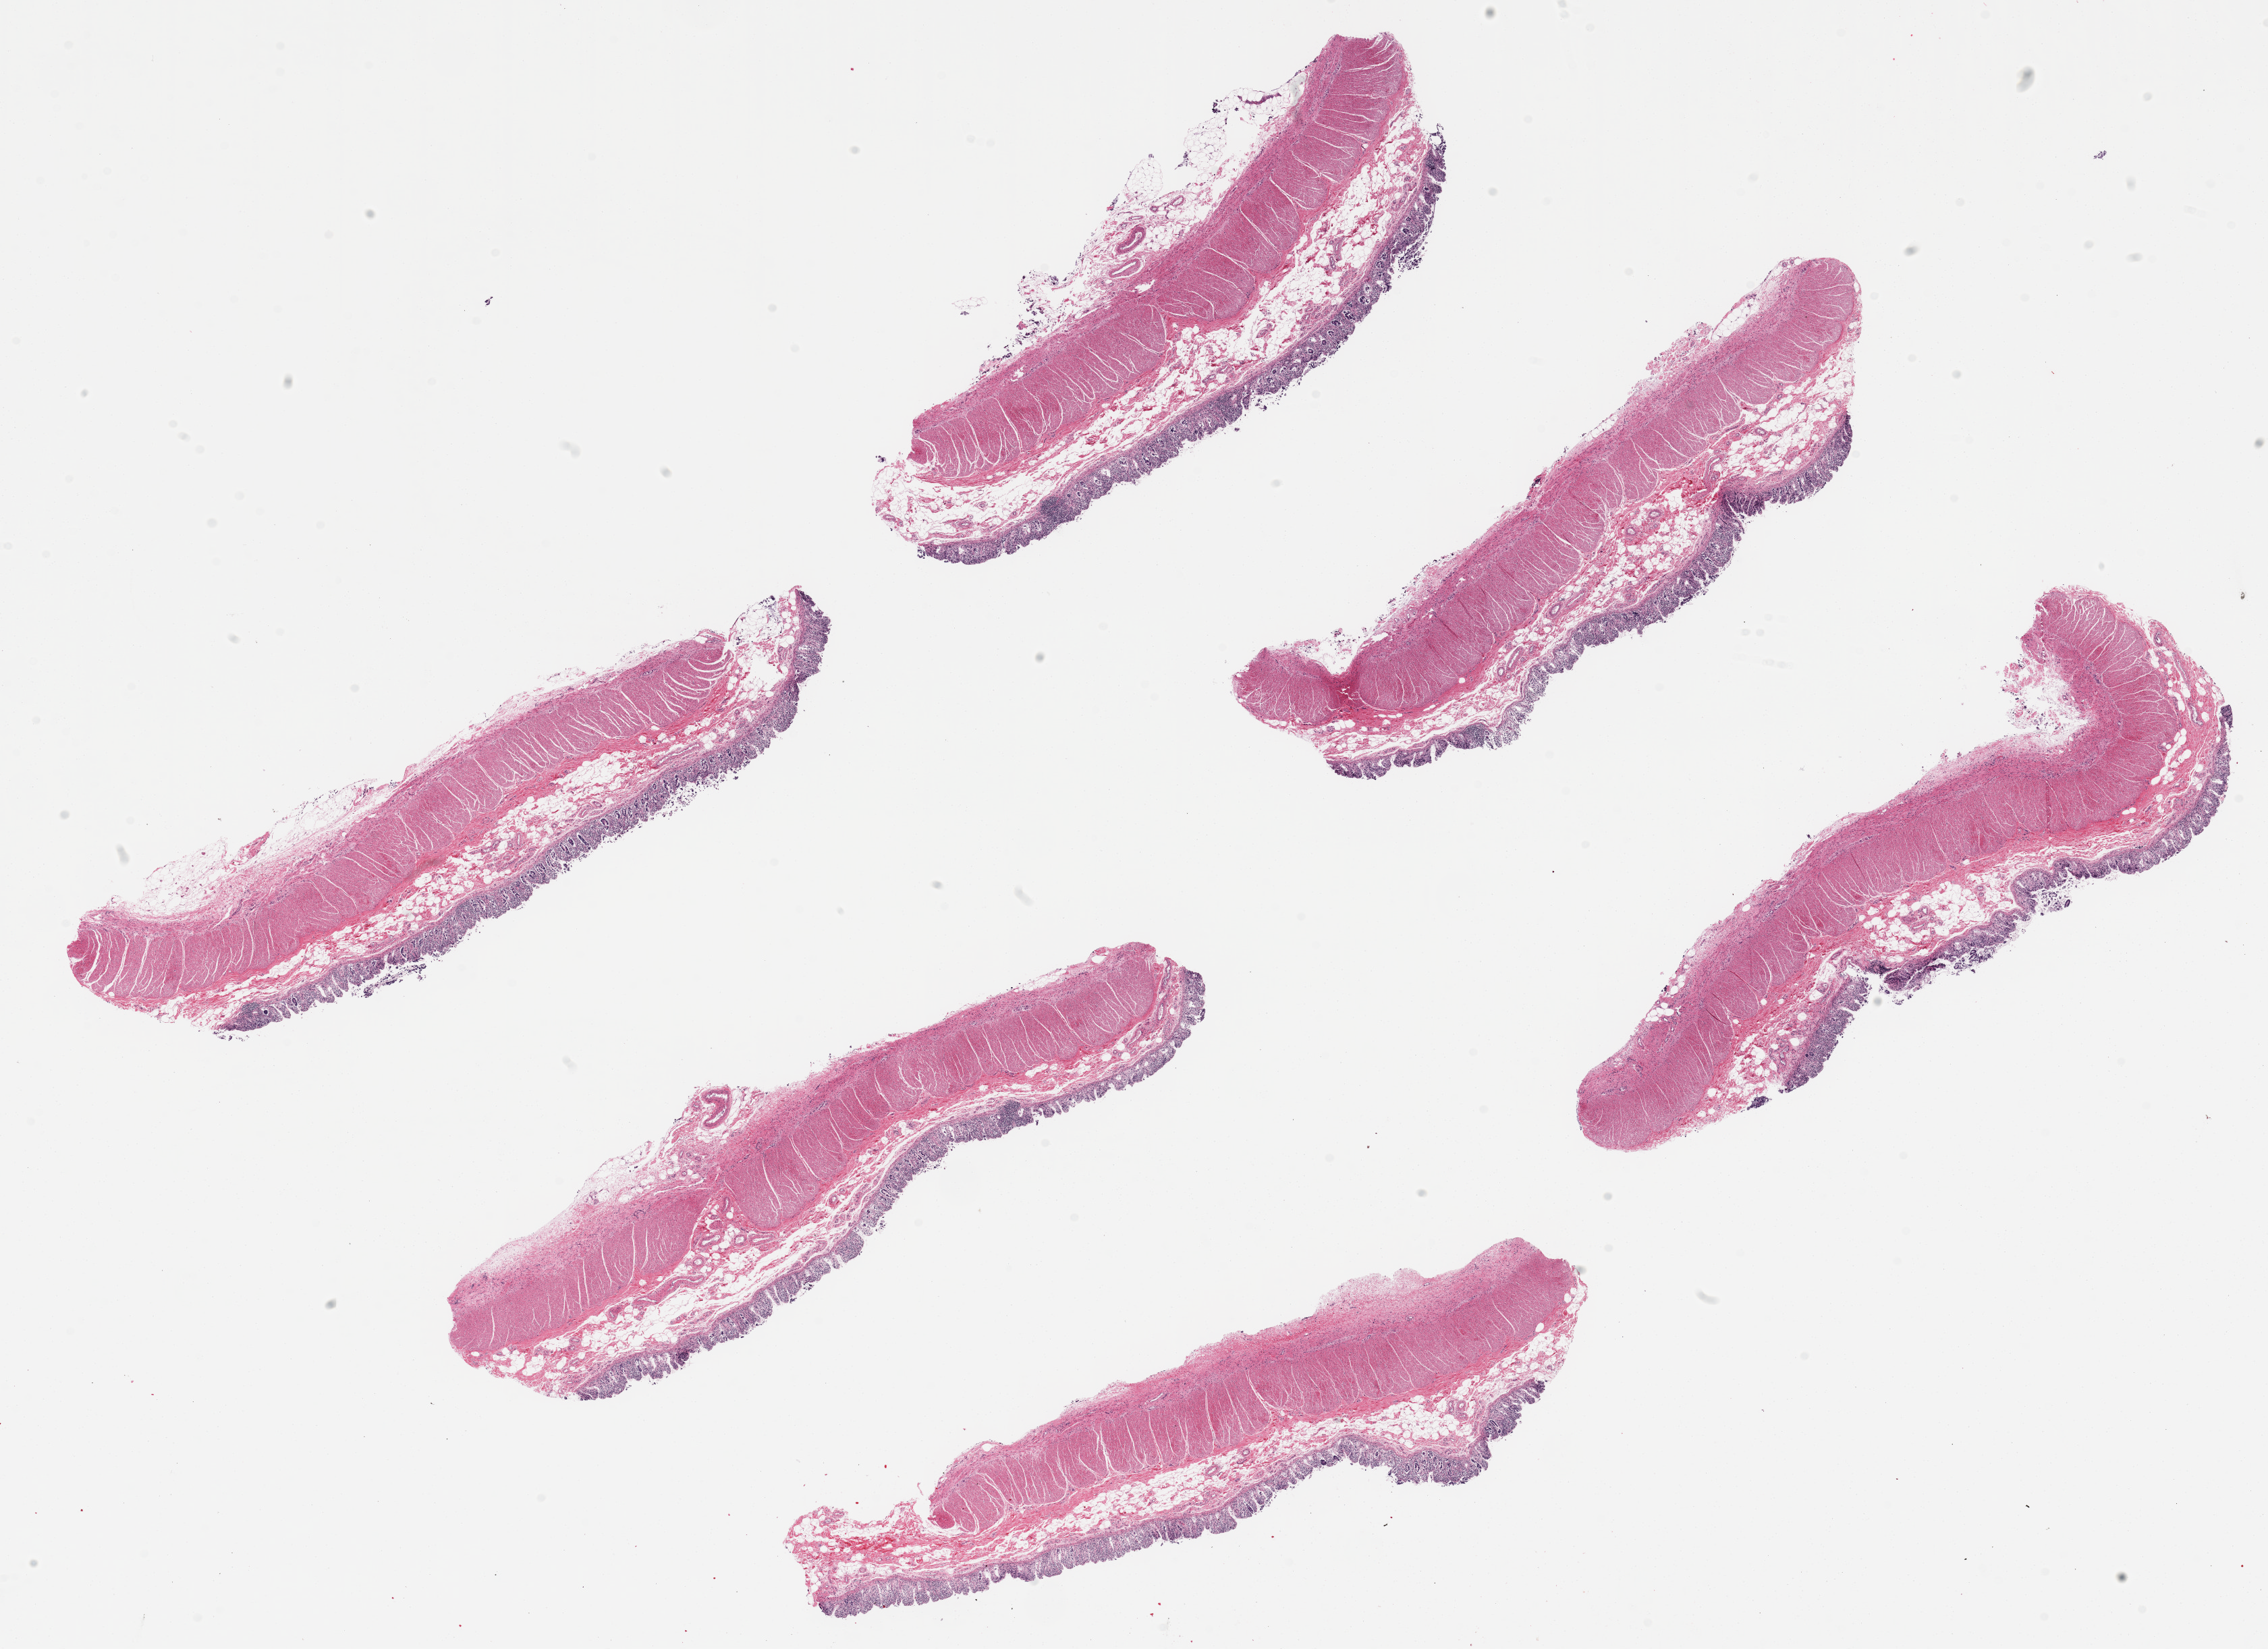
Haematoxylin and eosin whole-slide image, whole scanned area (about 26.6 x 19.3 mm) shown as a low-resolution overview. PAXgene-fixed paraffin-embedded (PFPE) section. Target tissue: transverse colon. Donor tissue sample. Donor sex: male.
* review note (as recorded): 6 ~9x2mm pieces. Epithelial component of mucosa badly autolyzed; mucosa is ~10% of thickness